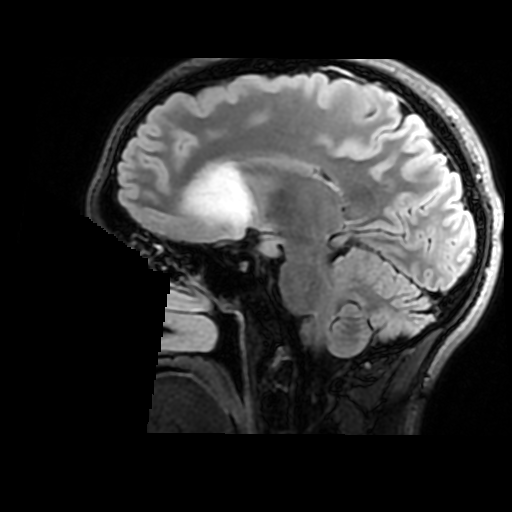
Brain MRI from a brain-tumour surgery series, one sagittal slice; position 99 of 176 along the scan axis; T2 FLAIR; 1 mm slice thickness; 512 × 512 image matrix, field of view 240 × 240 mm. Case-level facts recorded for this patient, not image findings: histopathology: Astrocytoma; WHO grade: 2; IDH mutation: yes.
Structures marked on this image (outlined manually by an expert reader):
- tumour: bounding box (x1, y1, x2, y2) in pixels: (185, 166, 253, 228)